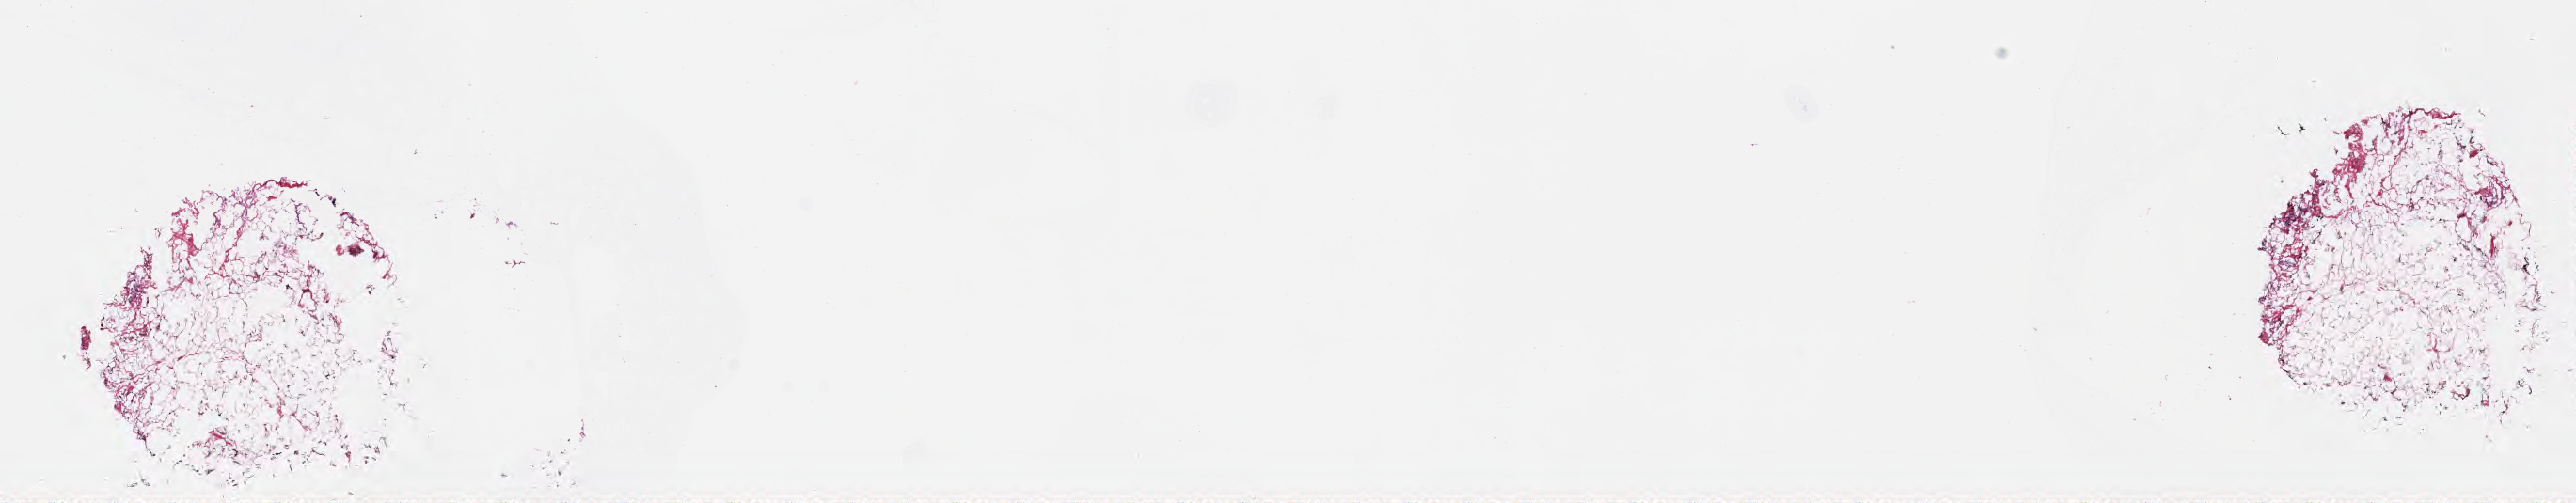
Whole-slide image, haematoxylin and eosin stain — whole scanned area (about 22.1 x 4.3 mm) shown as a low-resolution overview. Frozen section (tissue freezing medium). Specimen: primary tumor. Anatomic site: breast. Female, age 52 years at initial diagnosis. Slide review estimates, as recorded: tumor cells 40%, tumor nuclei 40%, stromal cells 50%, necrosis 0%, normal cells 10%. Infiltration values recorded for this section: lymphocyte infiltration 3%, monocyte infiltration 3%, neutrophil infiltration 7%.
* histologic diagnosis: Infiltrating duct carcinoma, NOS
* section: top of the tissue portion
* AJCC pathologic stage: Stage IIA